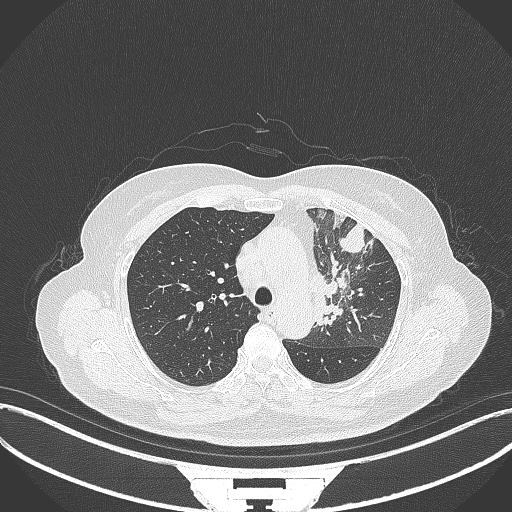
Chest CT, one axial slice. Position 242 of 382 along the scan axis. Reconstruction kernel B70f. Lung window (W 1500 / L -600 HU). 1 mm slice thickness. 512 × 512 image matrix, field of view 400 × 400 mm. Patient: female, 64 years. From the clinical record (not read from this slice): clinical TNM (as recorded): T2a N2 M0.
Structures marked on this image (rectangle marked by the reading radiologist):
- lung tumour (recorded histology: adenocarcinoma): bounding box [x1, y1, x2, y2] px = [315, 255, 351, 328]
- lung tumour (recorded histology: adenocarcinoma): [337, 220, 372, 255]